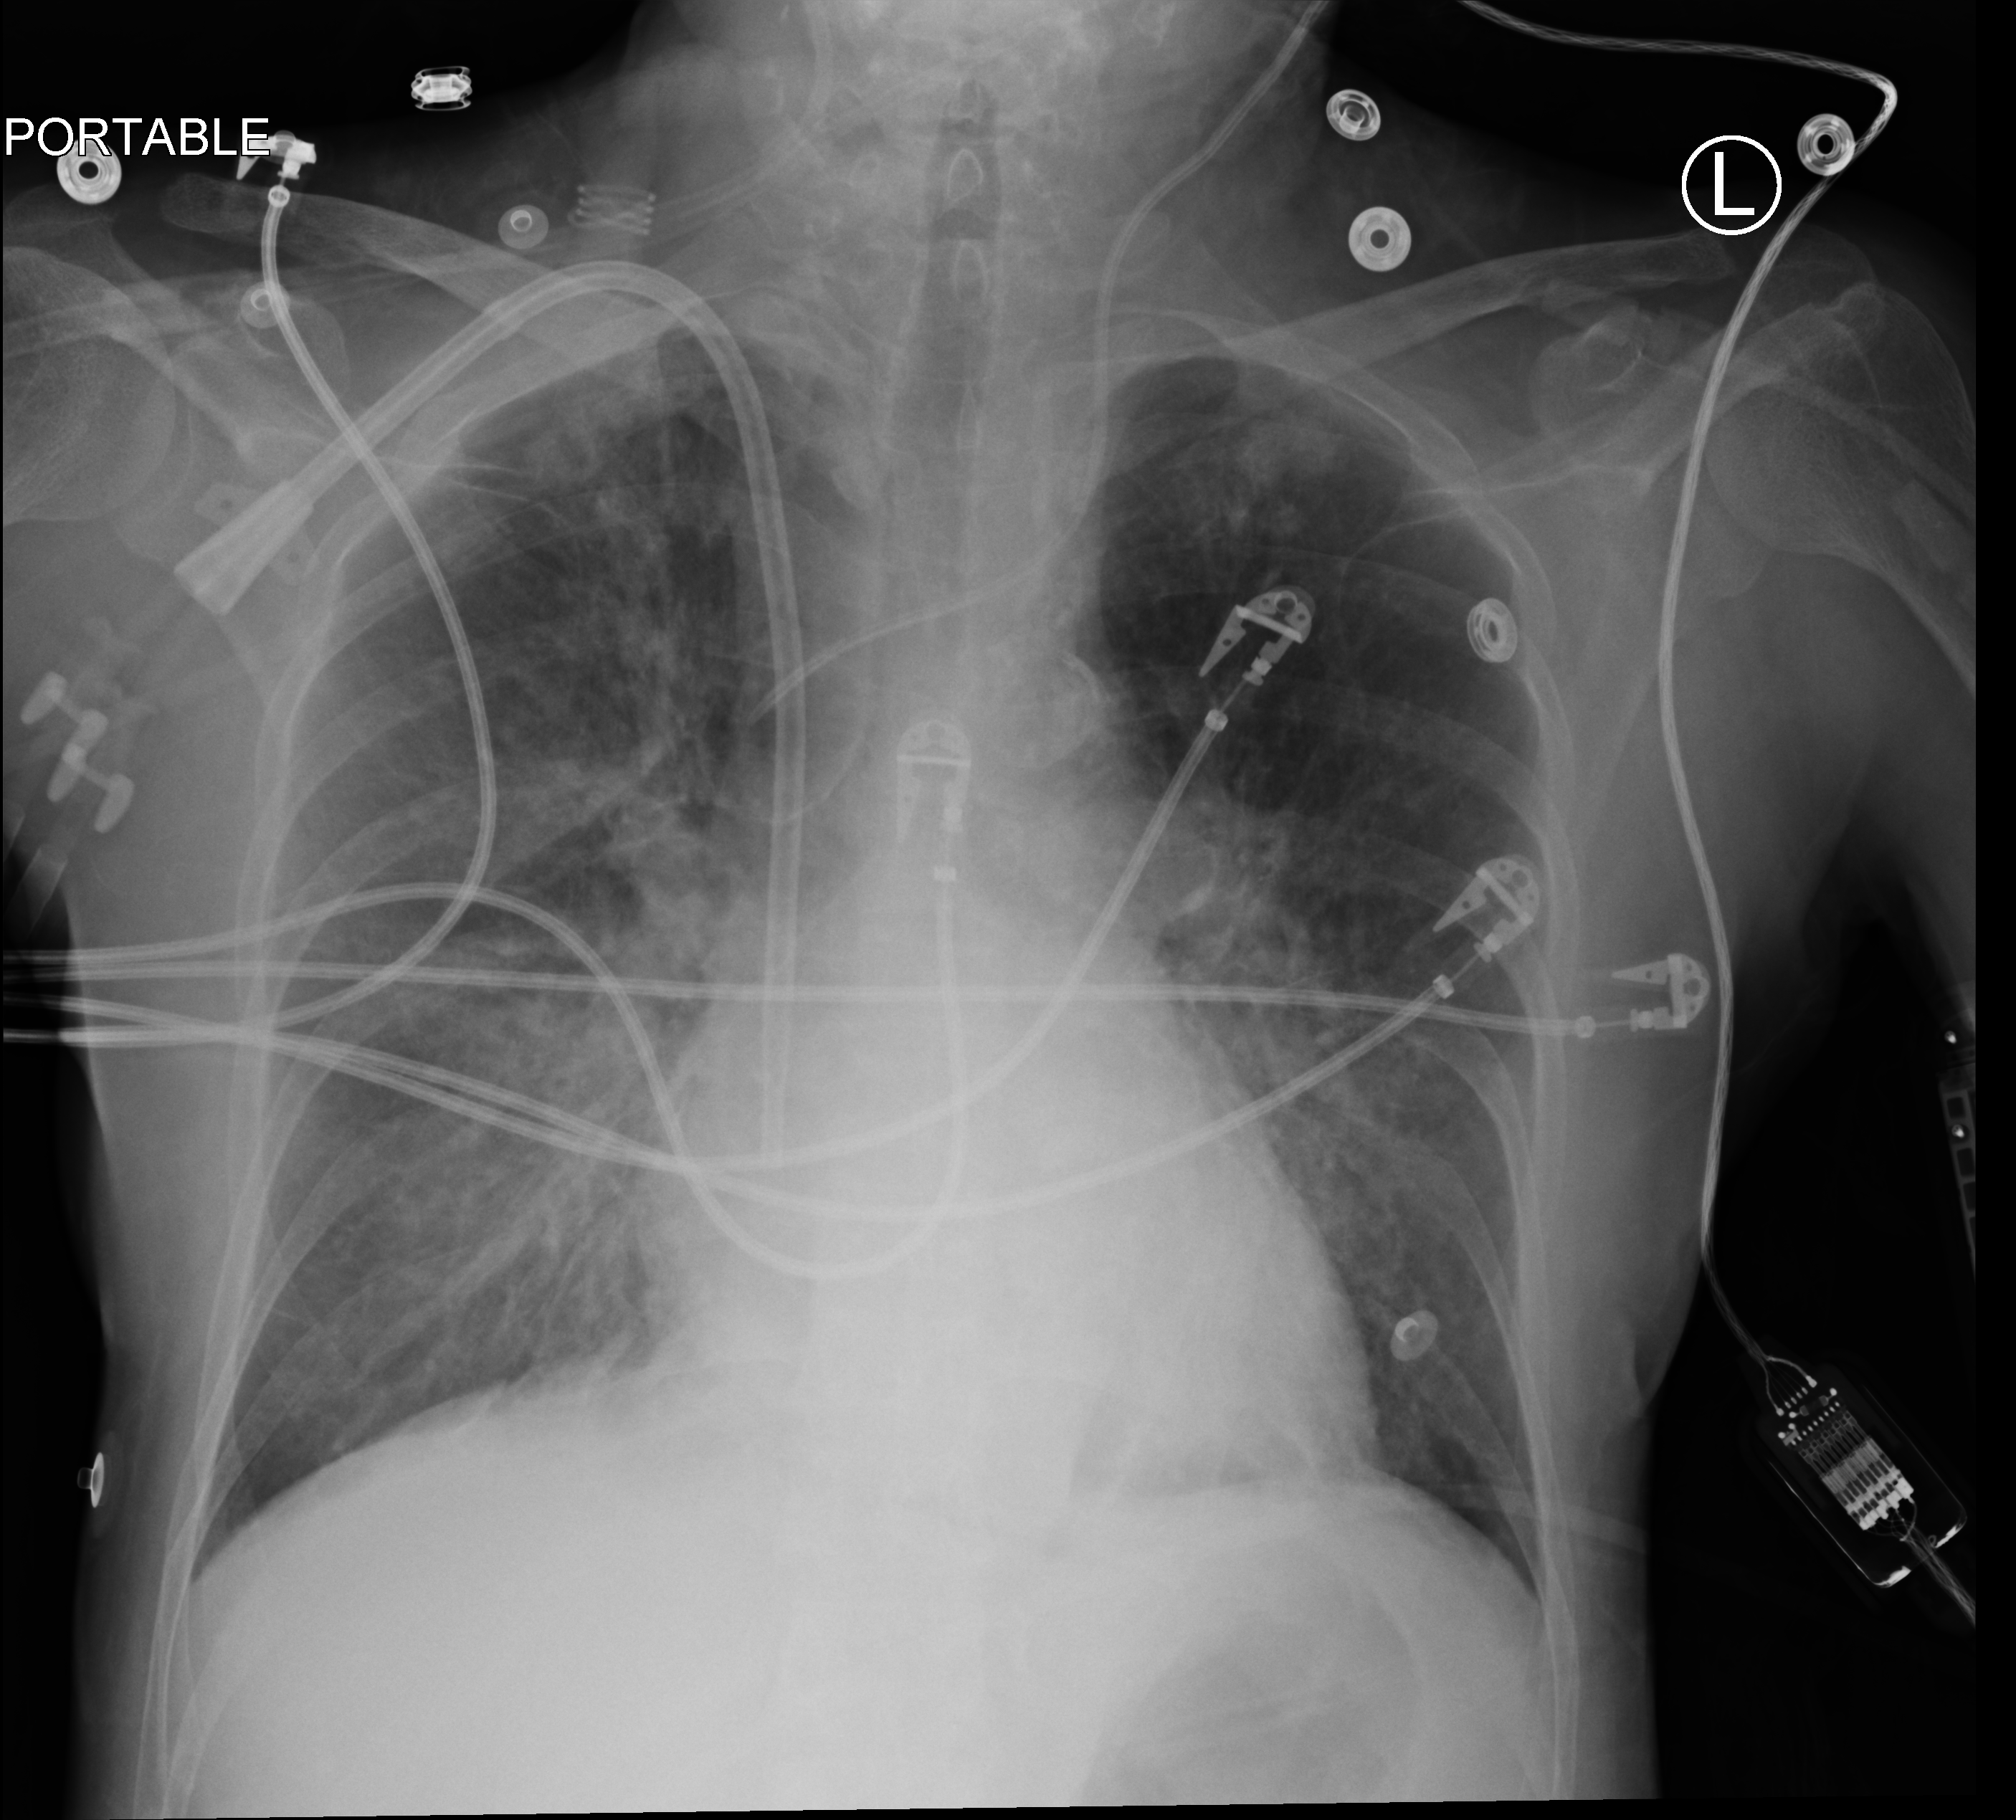
Portable chest radiograph; anteroposterior (AP) projection. Patient hospitalised with COVID-19; female, aged 18–59 years.
Hospital-stay facts (about this admission, not read from this image; timing relative to this image not recorded): admitted to intensive care during this hospital stay: no; mechanically ventilated during this hospital stay: no.